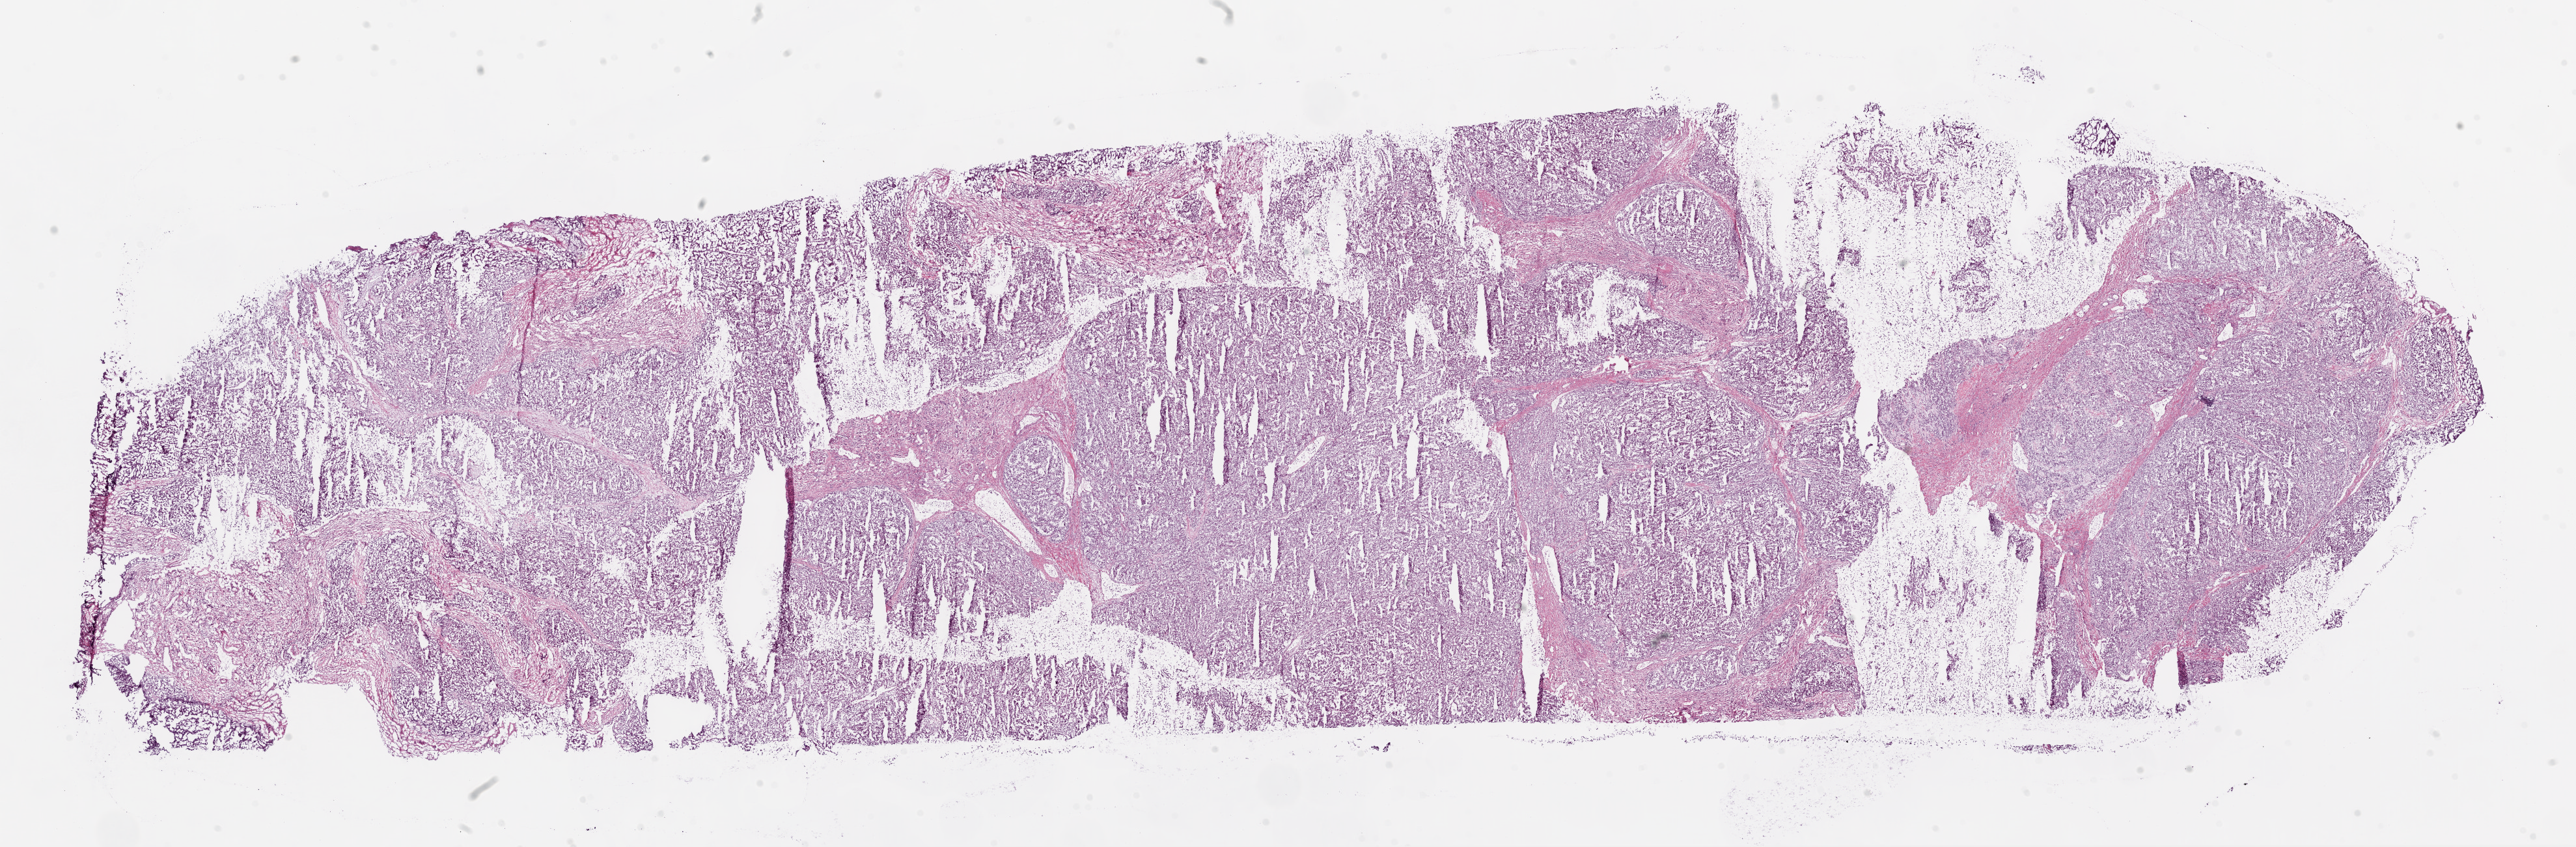
Whole-slide histology image, Hematoxylin and eosin (H&E) stained — low-resolution overview of the scanned area, about 31.9 x 10.5 mm (from a 20x scan), frozen section, primary tumour sample from the kidney. Female patient; age at initial diagnosis 65 years. Histologic grade: G4 (undifferentiated). Composition of this section per pathologist review: tumour cells 85%, tumour nuclei 85%, normal cells 0%, stromal cells 15%, necrosis 0%.
AJCC pathologic stage: IV. Histologic diagnosis: Clear cell adenocarcinoma, NOS.